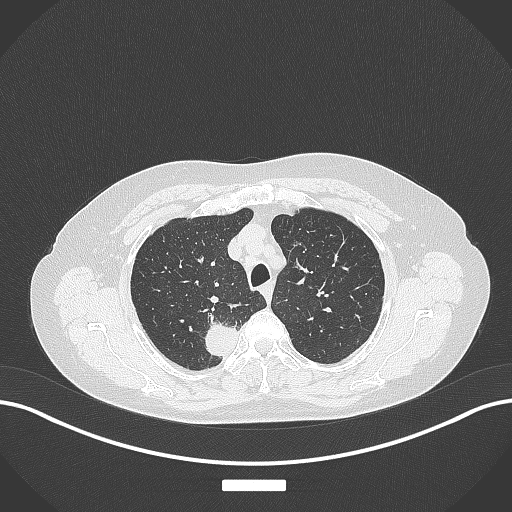
Chest CT, one axial slice; position 310 of 357 along the scan axis; reconstruction kernel B70f; 120 kVp; lung window (W 1500 / L -600 HU); 1 mm slice thickness; 512 × 512 image matrix, field of view 400 × 400 mm. Patient: female, 62 years. Case-level facts recorded for this patient, not image findings: clinical TNM (as recorded): T1c N1 M0.
Structures marked on this image (rectangle marked by the reading radiologist):
- lung tumour (recorded histology: squamous cell carcinoma): bounding box (x1, y1, x2, y2) in pixels: (201, 311, 240, 365)